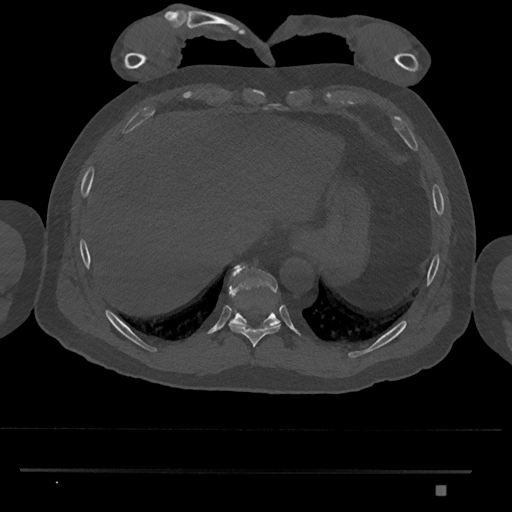
CT including the spine, one axial slice; slice 1034 of 1134 in the series (ordered by position); reconstruction kernel Br40s/3; bone window (W 1800 / L 400 HU); 512 × 512 image matrix, field of view 429 × 429 mm. Male patient, age 65 years. From the clinical record (not read from this slice): primary cancer: prostate.
Structures marked on this image (semi-automatic segmentation, software-assisted and operator-edited):
- T10 vertebra: box from (x=229, y=264) to (x=280, y=328) px
- T9 vertebra: (x=229, y=307)–(x=281, y=347)